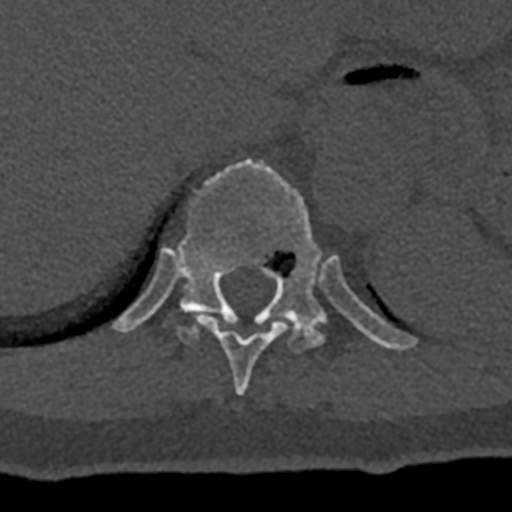
CT including the spine, one axial slice. Slice 570 of 797 in the series (ordered by position). Bone window (W 1800 / L 400 HU). 0.5 mm slice thickness. 512 × 512 image matrix, field of view 160 × 160 mm. Male patient, age 74 years. From the clinical record (not read from this slice): primary cancer: renal.
Structures marked on this image (semi-automatic segmentation, software-assisted and operator-edited):
- T10 vertebra: box from (x=194, y=315) to (x=289, y=395) px
- T11 vertebra: (x=113, y=158)–(x=416, y=352)